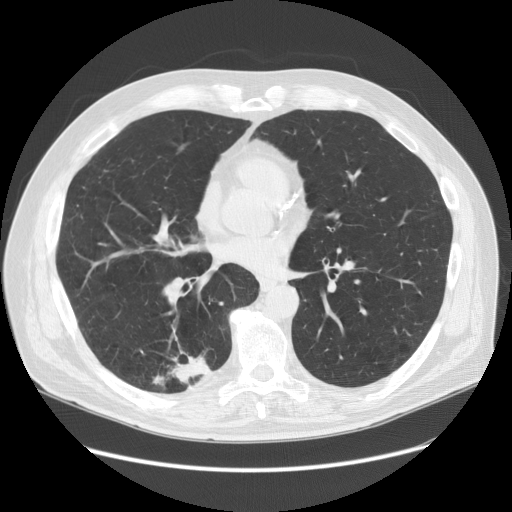
Low-dose screening chest CT, one axial slice; position 69 of 149 along the scan axis; reconstruction kernel STANDARD; 120 kVp; lung window (W 1500 / L -600 HU); 2.5 mm slice thickness; 512 × 512 image matrix, field of view 400 × 400 mm.
Structures marked on this image (expert manual segmentation):
- lesion 1 (tumor, lower lobe of right lung): bounding box <153,350,211,389> (left, top, right, bottom; pixels)